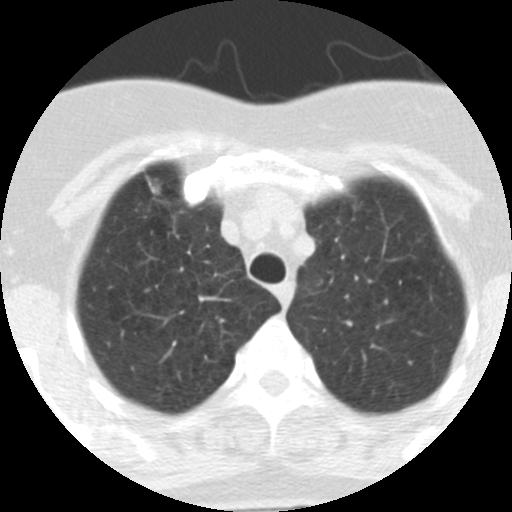
Chest CT (low-dose screening protocol), one axial image. Baseline annual screen. Lung window (W 1500 / L -600 HU). Female participant, aged 62 years at enrolment. Current smoker at enrolment.
Expert reader's lesion annotation, bounding box <116,172,192,239> (left, top, right, bottom; pixels). Screening reader's record for this exam (one nodule recorded; not confirmed to be the boxed lesion): non-calcified nodule or mass ≥4 mm, right upper lobe, 9 × 7 mm, spiculated (stellate) margins, soft tissue attenuation. Official screen result: positive, change unspecified: nodule(s) >= 4 mm or enlarging nodule(s), mass(es), or other non-specific abnormalities suspicious for lung cancer.